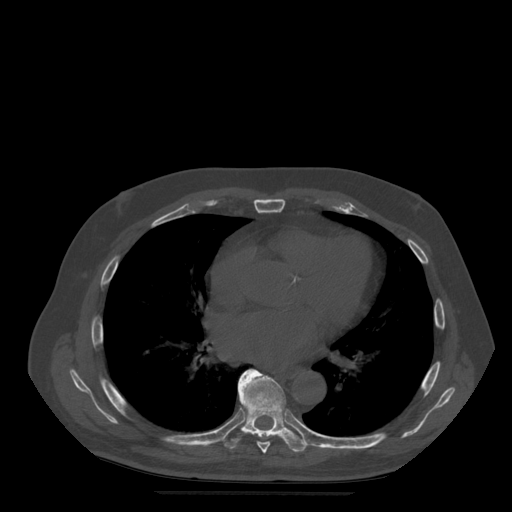
CT including the spine, one axial slice; position 321 of 522 along the scan axis; bone window (W 1800 / L 400 HU); 1.25 mm slice thickness; 512 × 512 image matrix. Patient age 72 years. Case-level facts recorded for this patient, not image findings: primary cancer: prostate.
Annotated regions visible in this slice (semi-automatically segmented with operator editing):
- T7 vertebra: bounding box <239,388,271,454> (left, top, right, bottom; pixels)
- T8 vertebra: <225,369,309,452>